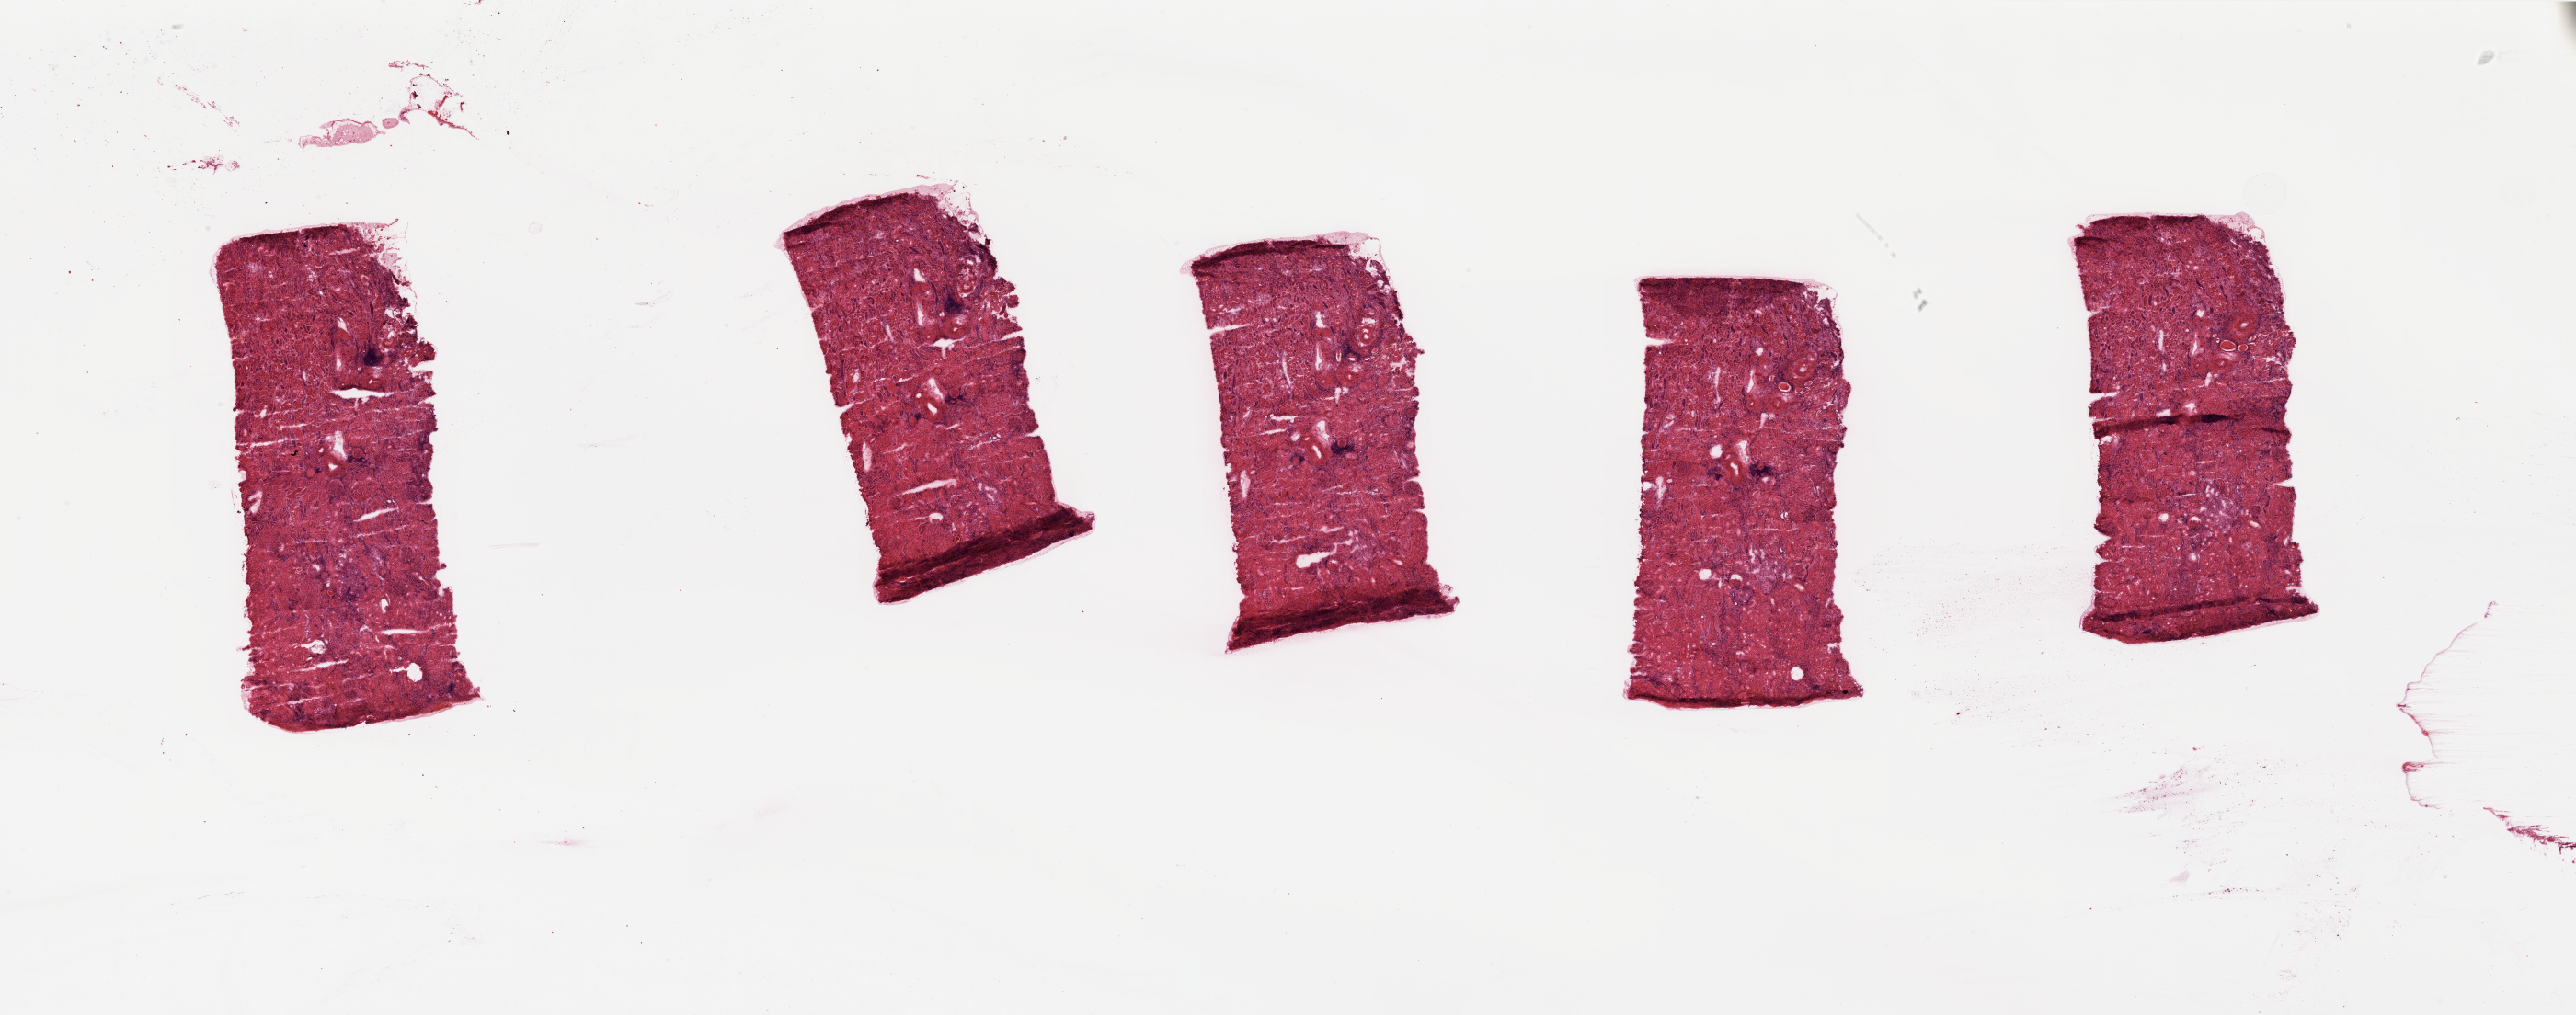
Digitized H&E-stained tissue section (whole slide) — shown as a low-resolution overview of the whole scanned area (about 44.3 x 17.5 mm, from a 20x scan). Normal (non-tumour) tissue sample, sampled site: kidney. Male, 66 y/o.
This section: normal (non-tumour) tissue from the same patient. Patient diagnosis: Renal cell carcinoma, NOS.